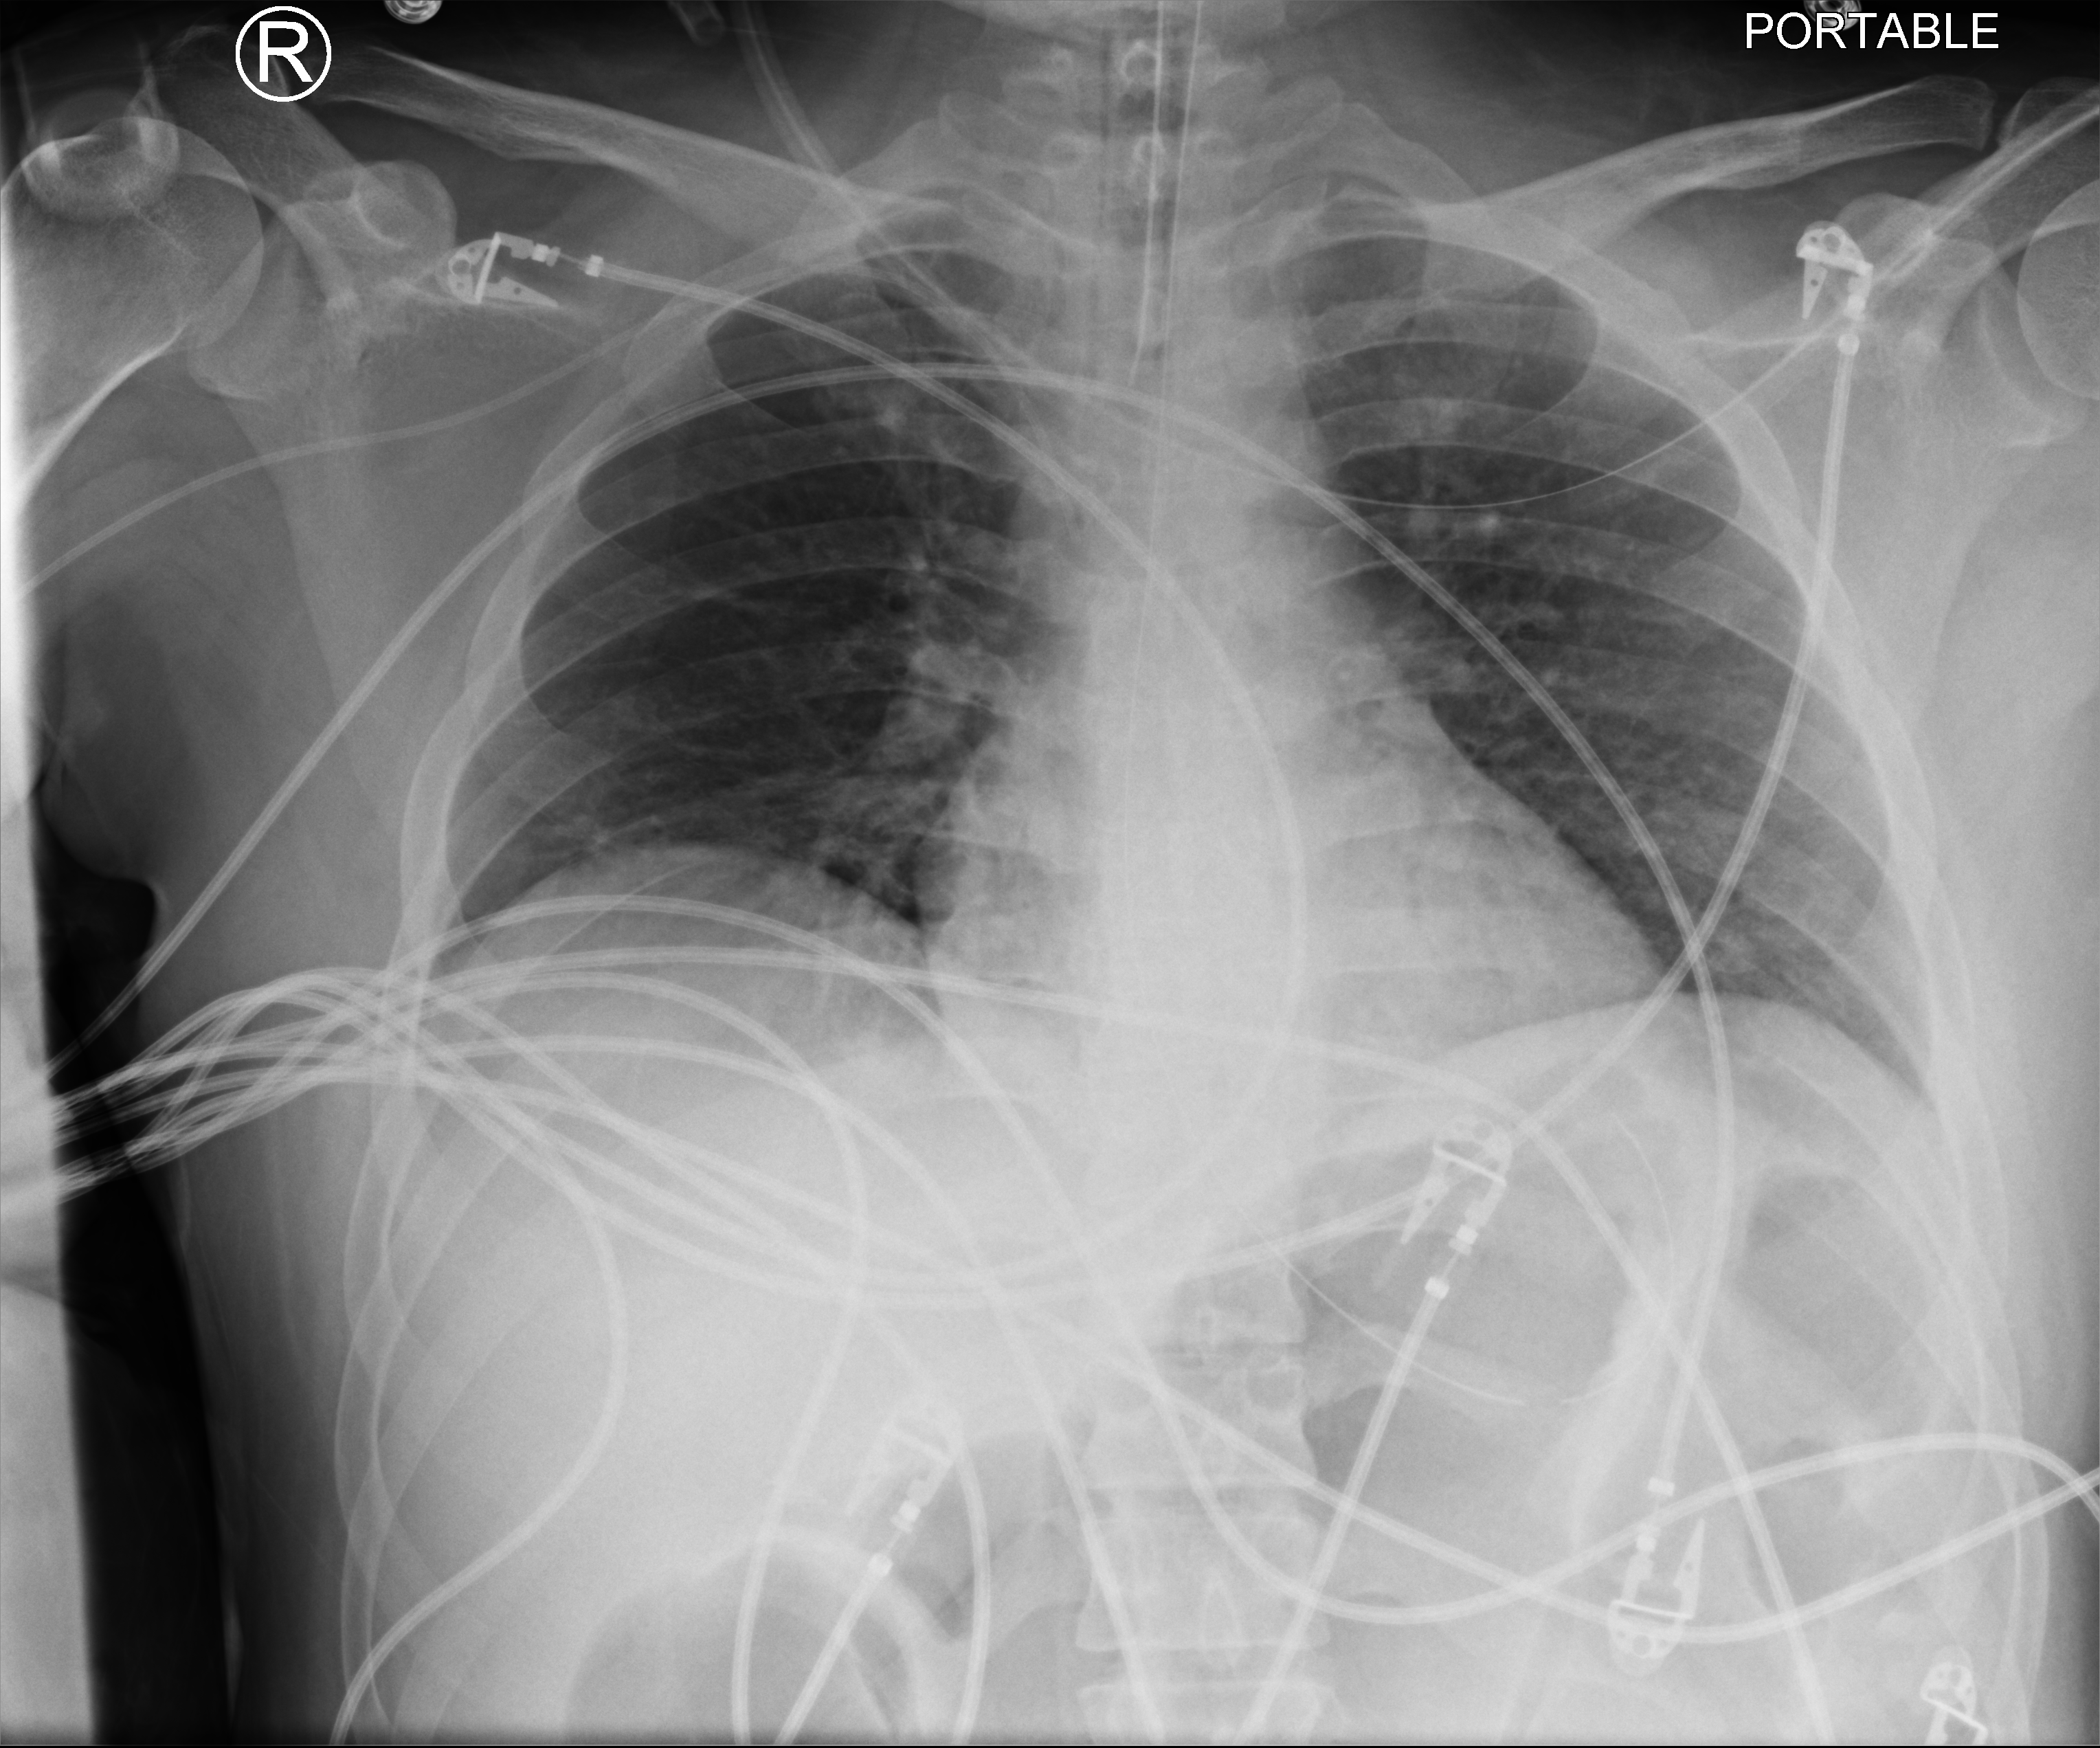
Bedside chest radiograph (computed radiography); anteroposterior (AP) projection. Male patient hospitalised with COVID-19, age 18–59 years.
Hospital-stay facts (about this admission, not read from this image; timing relative to this image not recorded): other chronic lung disease (admission record): no.